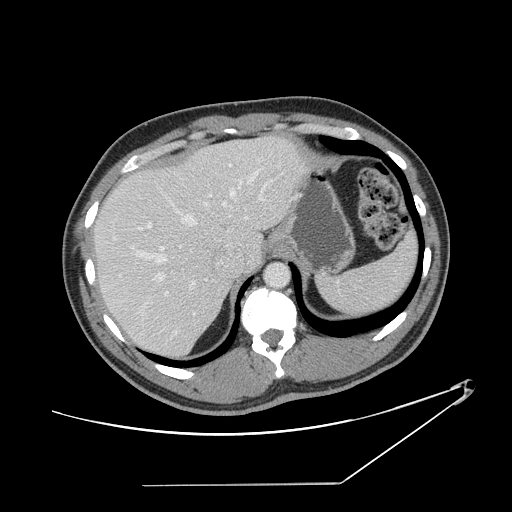
Contrast-enhanced abdominal CT, one axial slice. Slice 111 of 152 in the series (ordered by position). 120 kVp. Intravenous contrast given. Soft-tissue window (W 400 / L 40 HU). 2.5 mm slice thickness. 512 × 512 image matrix, field of view 432 × 432 mm. Male patient, age 45 years. Case-level facts recorded for this patient, not image findings: diagnosis: colorectal cancer liver metastases, imaged before liver resection; multiple liver metastases: no; largest metastasis: 1 cm.
Outlined on this slice (expert manual segmentation):
- hepatic veins: box from (x=111, y=168) to (x=263, y=289) px
- liver: (x=95, y=136)–(x=300, y=359)
- planned liver remnant (the part of the liver to remain after resection): (x=95, y=157)–(x=234, y=359)
- portal vein (with intrahepatic branches): (x=160, y=165)–(x=266, y=316)